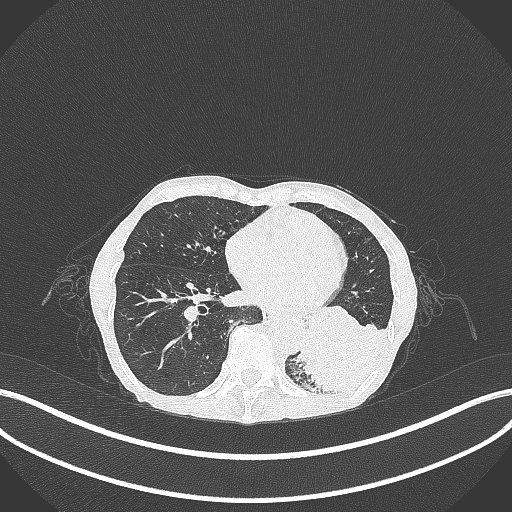
Chest CT, one axial slice; slice 94 of 347 in the series (ordered by position); 120 kVp; lung window (W 1500 / L -600 HU); 512 × 512 image matrix, field of view 400 × 400 mm. Patient: female, 70 years. Case-level facts recorded for this patient, not image findings: clinical TNM (as recorded): T3 N0 M0.
Outlined on this slice (rectangle marked by the reading radiologist):
- lung tumour (recorded histology: small cell carcinoma): bounding box (x1, y1, x2, y2) in pixels: (290, 316, 395, 392)